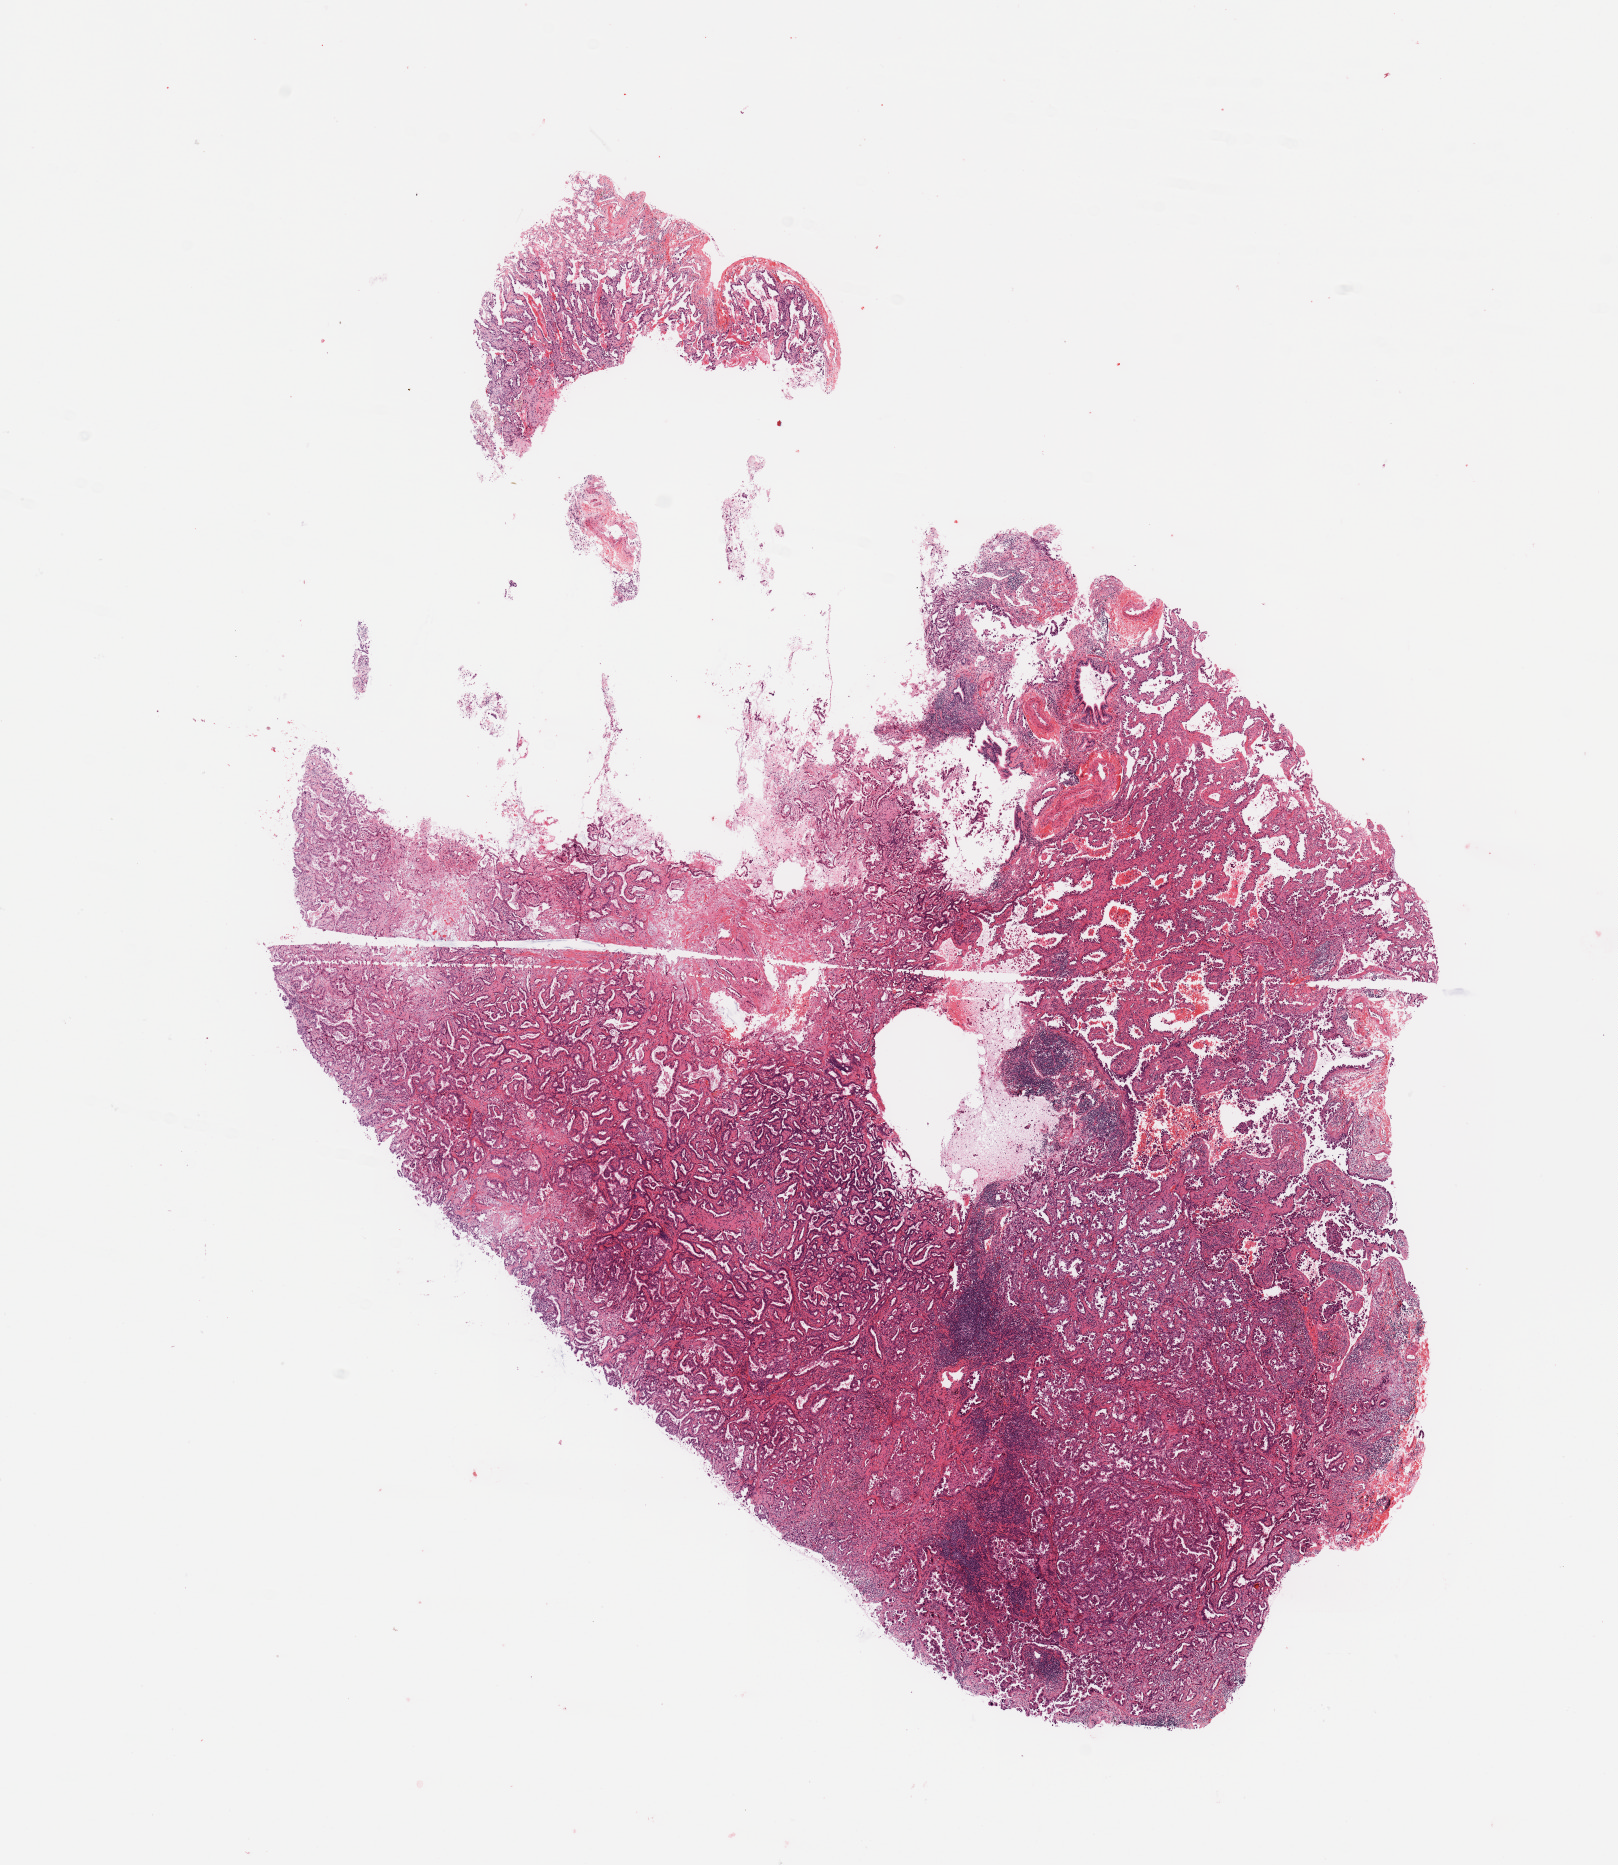
Whole-slide histology image, Hematoxylin and eosin (H&E) stained — low-resolution overview of the scanned area, about 12.8 x 14.8 mm (acquisition: 20x scan). Tumour tissue sample, sampled site: lung. Patient: female, age 46 years. Histologic grade: G2 (moderately differentiated). Composition of this section per pathologist review: tumour nuclei 70%, necrosis 3%.
Primary tumour site (as recorded): right lower lobe. AJCC pathologic stage: IIA. Histologic diagnosis: Adenocarcinoma, NOS.